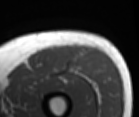
MRI of an extremity soft-tissue mass, one axial slice; slice 37 of 86 in the series (ordered by position); MR volume resampled by the dataset authors to the PET/CT grid (not the native acquisition matrix); 139 × 117 image matrix. Male patient. Case-level facts recorded for this patient, not image findings: histological type: extraskeletal osteosarcoma; grade: high; site of the primary tumour: thigh.
Structures marked on this image (expert contour drawn on MRI and transferred to this co-registered scan by the dataset authors):
- gross tumour volume (mass): bounding box (x1, y1, x2, y2) in pixels: (67, 48, 82, 74)